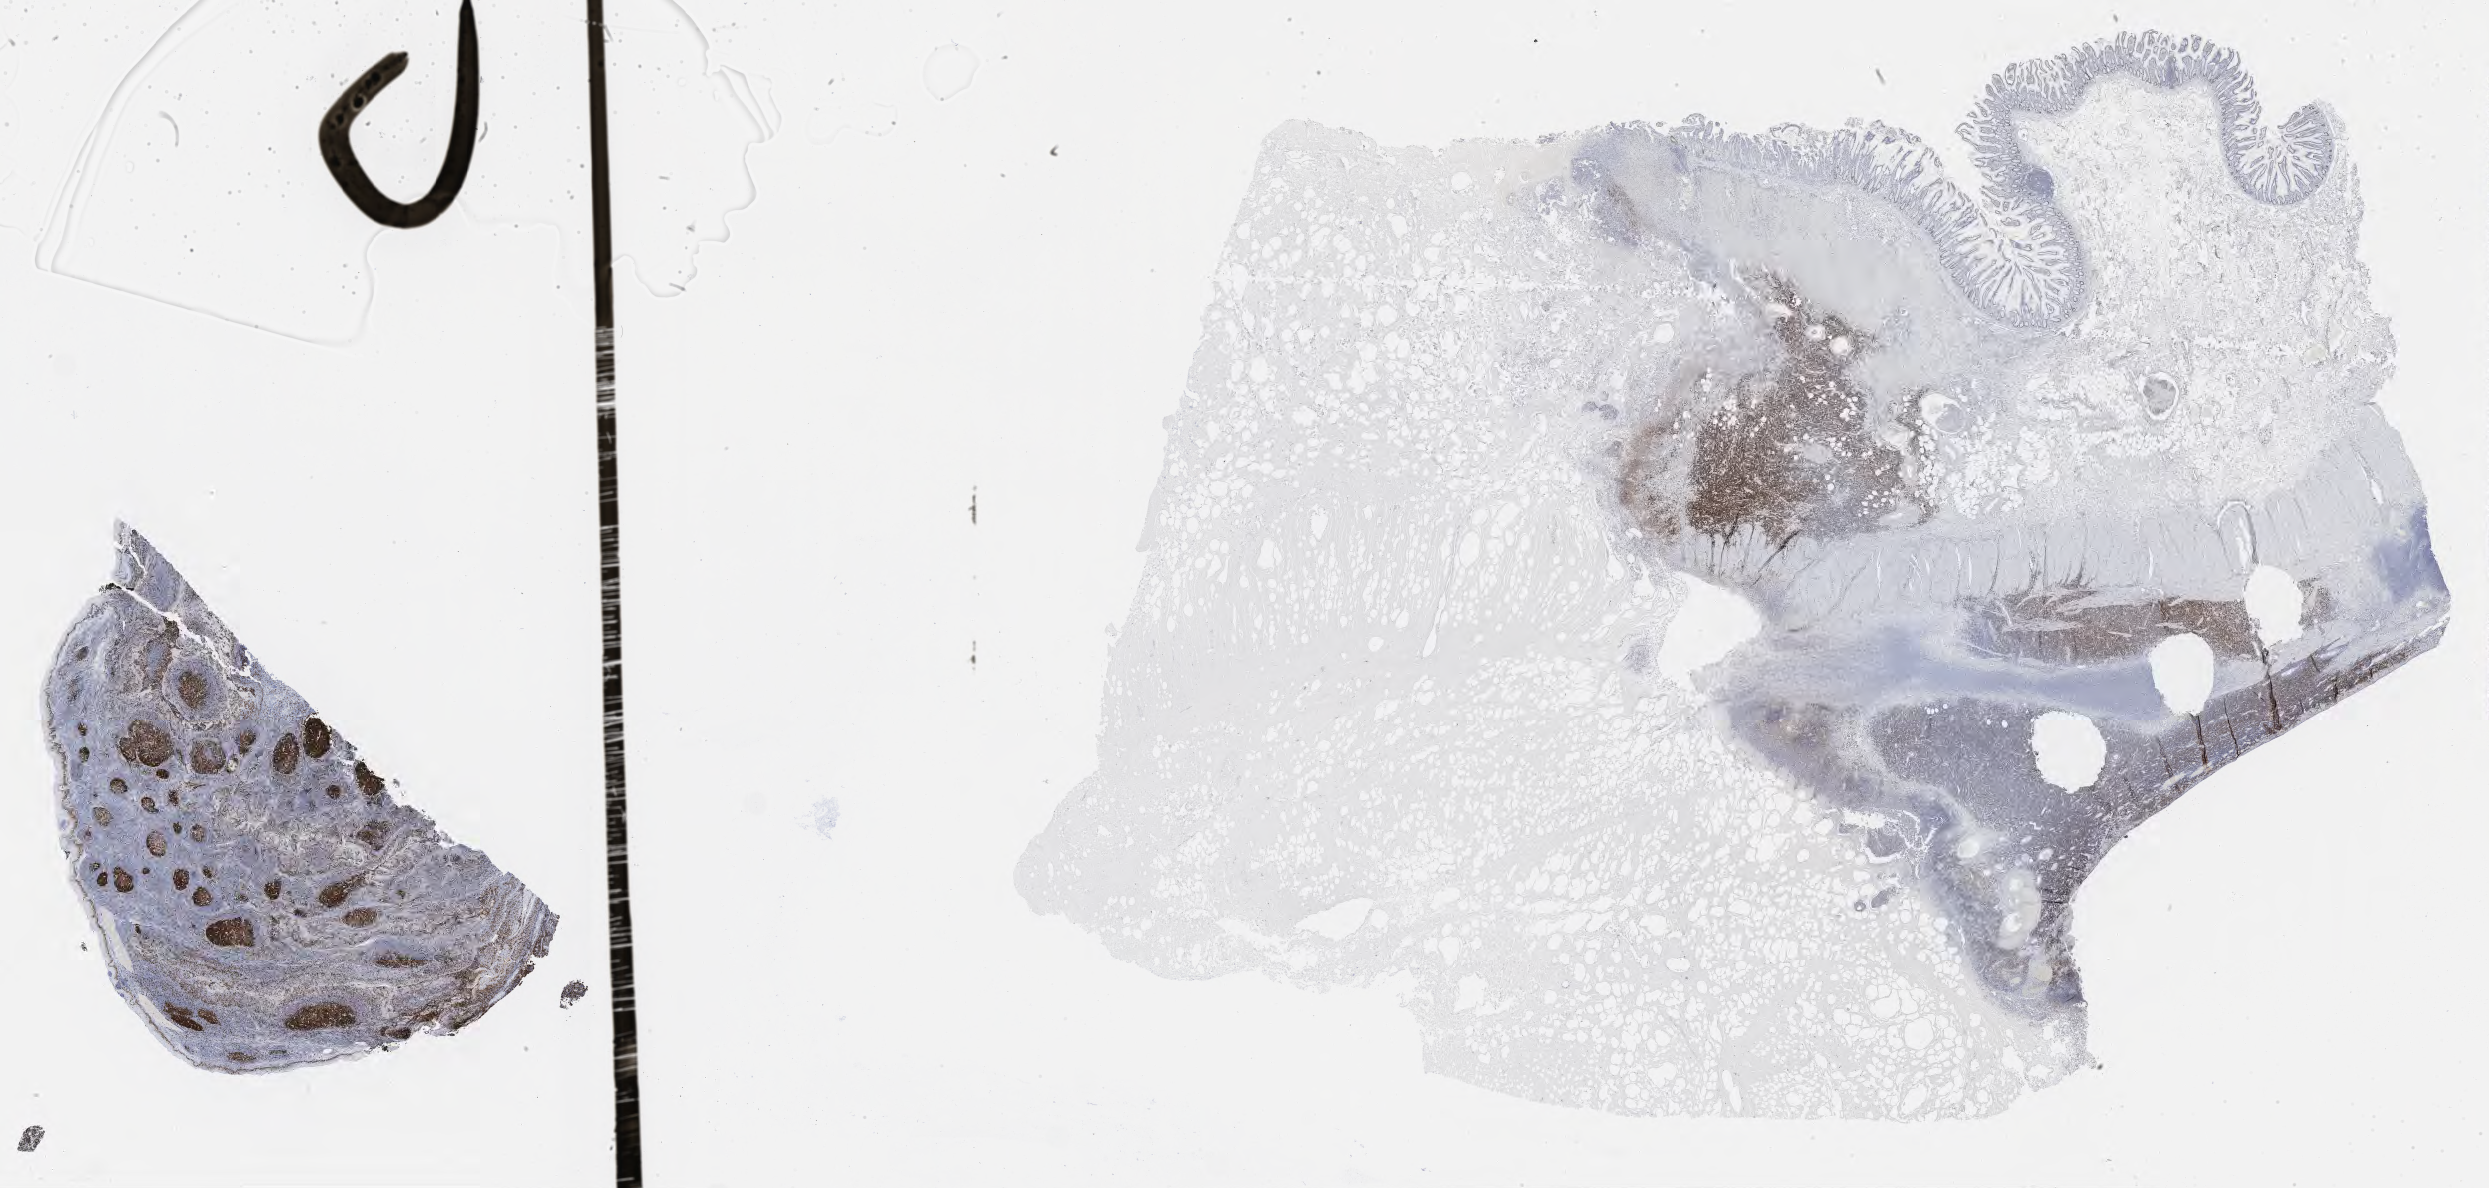
IHC for Ki-67, whole-slide image, a low-resolution overview of the entire scanned area, about 40.3 x 19.2 mm. Tumor tissue. Site: colon. Patient: male, 62 years old.
Diagnosis: Burkitt lymphoma, NOS.